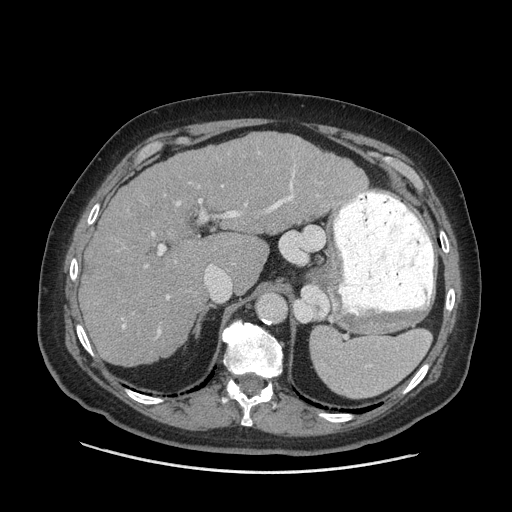
Contrast-enhanced abdominal CT (liver protocol), one axial slice; 140 kVp; soft-tissue window (W 400 / L 40 HU); 512 × 512 image matrix, field of view 420 × 420 mm. Case-level facts recorded for this patient, not image findings: diagnosis: hepatocellular carcinoma (patient treated with transarterial chemoembolisation; whether this scan precedes or follows treatment is not stated here); TNM stage (as recorded): Stage-I; Child-Pugh class: A; tumour differentiation: well differentiated; tumour nodularity: uninodular.
Structures marked on this image (semi-automatic segmentation, software-assisted and operator-edited):
- liver parenchyma outside the tumour (the mass and vessels are separate outlines, so this box may not span the whole liver): bounding box (x1, y1, x2, y2) in pixels: (80, 132, 368, 366)
- liver vessels: (122, 171, 362, 336)